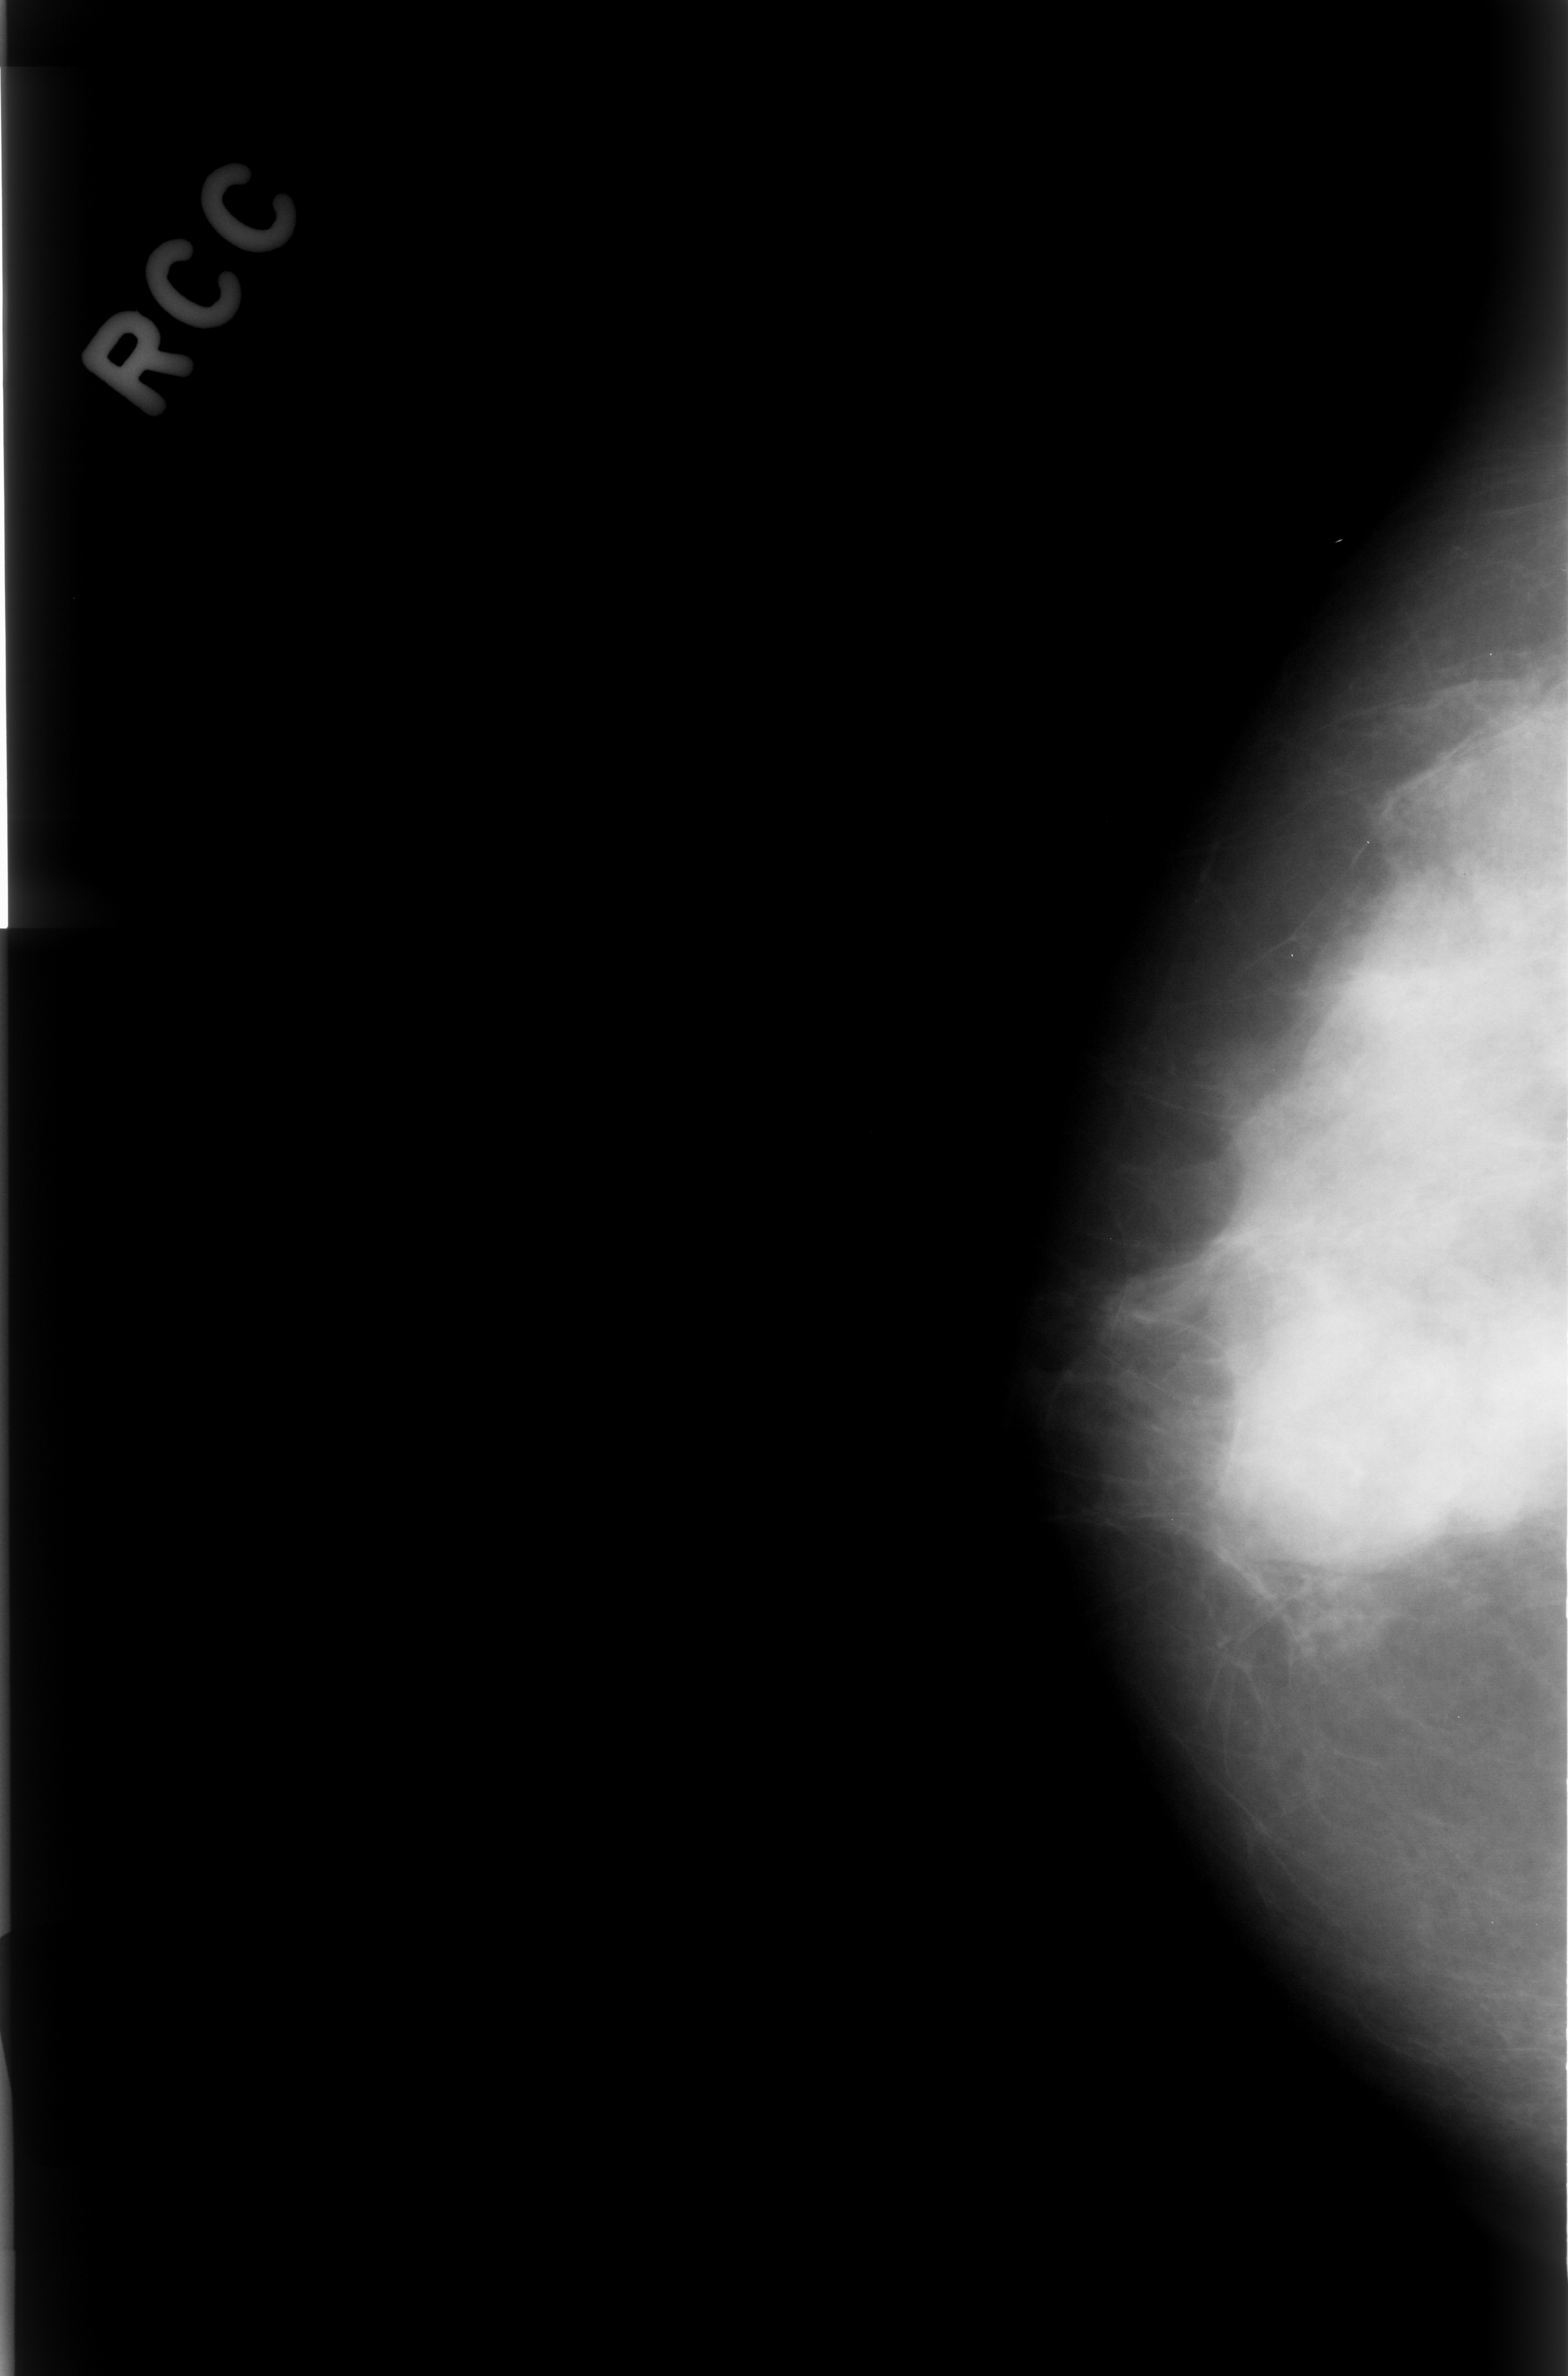
Scanned film-screen mammogram; right breast; craniocaudal (CC) view; BI-RADS breast density category 4 (scale 1–4); 1568 × 2376 image matrix.
Marked abnormalities (boxes around the expert regions of interest):
- mass, shape lobulated, margins obscured; BI-RADS assessment category 3; subtlety rating 4 on a 1 (subtle) to 5 (obvious) scale; pathology result (as recorded, not read from the image): benign: bounding box <1204,1329,1458,1590> (left, top, right, bottom; pixels)